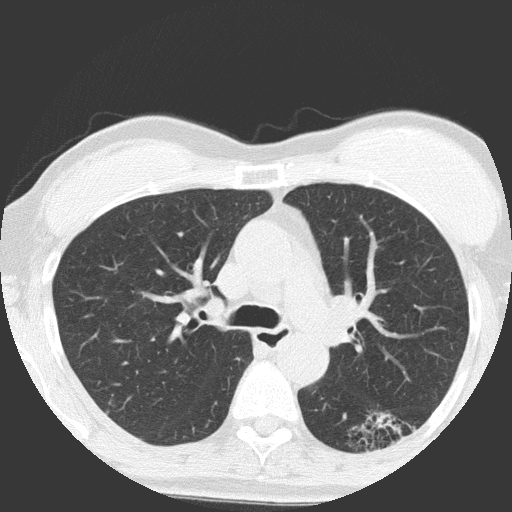
Chest CT (low-dose screening protocol), one axial image; baseline screening round; lung window (W 1500 / L -600 HU); lung (sharp) reconstruction kernel (FC51); 120 kVp; slice 52 of 149 in the series. Female participant, aged 64 years at enrolment. Former smoker at enrolment.
Expert reader's lesion annotation, box from (x=335, y=395) to (x=423, y=466) px. Screening reader's record for this exam (one nodule recorded; not confirmed to be the boxed lesion): non-calcified nodule or mass ≥4 mm, right upper lobe, 4 × 4 mm, poorly defined margins, ground glass attenuation. Note: the box lies in the patient's left hemithorax on this image, whereas the reader's record names the right lung; they may be different findings. Official screen result: positive, change unspecified: nodule(s) >= 4 mm or enlarging nodule(s), mass(es), or other non-specific abnormalities suspicious for lung cancer. Later outcome: lung cancer diagnosed 932 days after this screen — adenocarcinoma, NOS, left lower lobe, moderately differentiated (G2), stage IA (AJCC 6th edition), 17 mm at pathology.